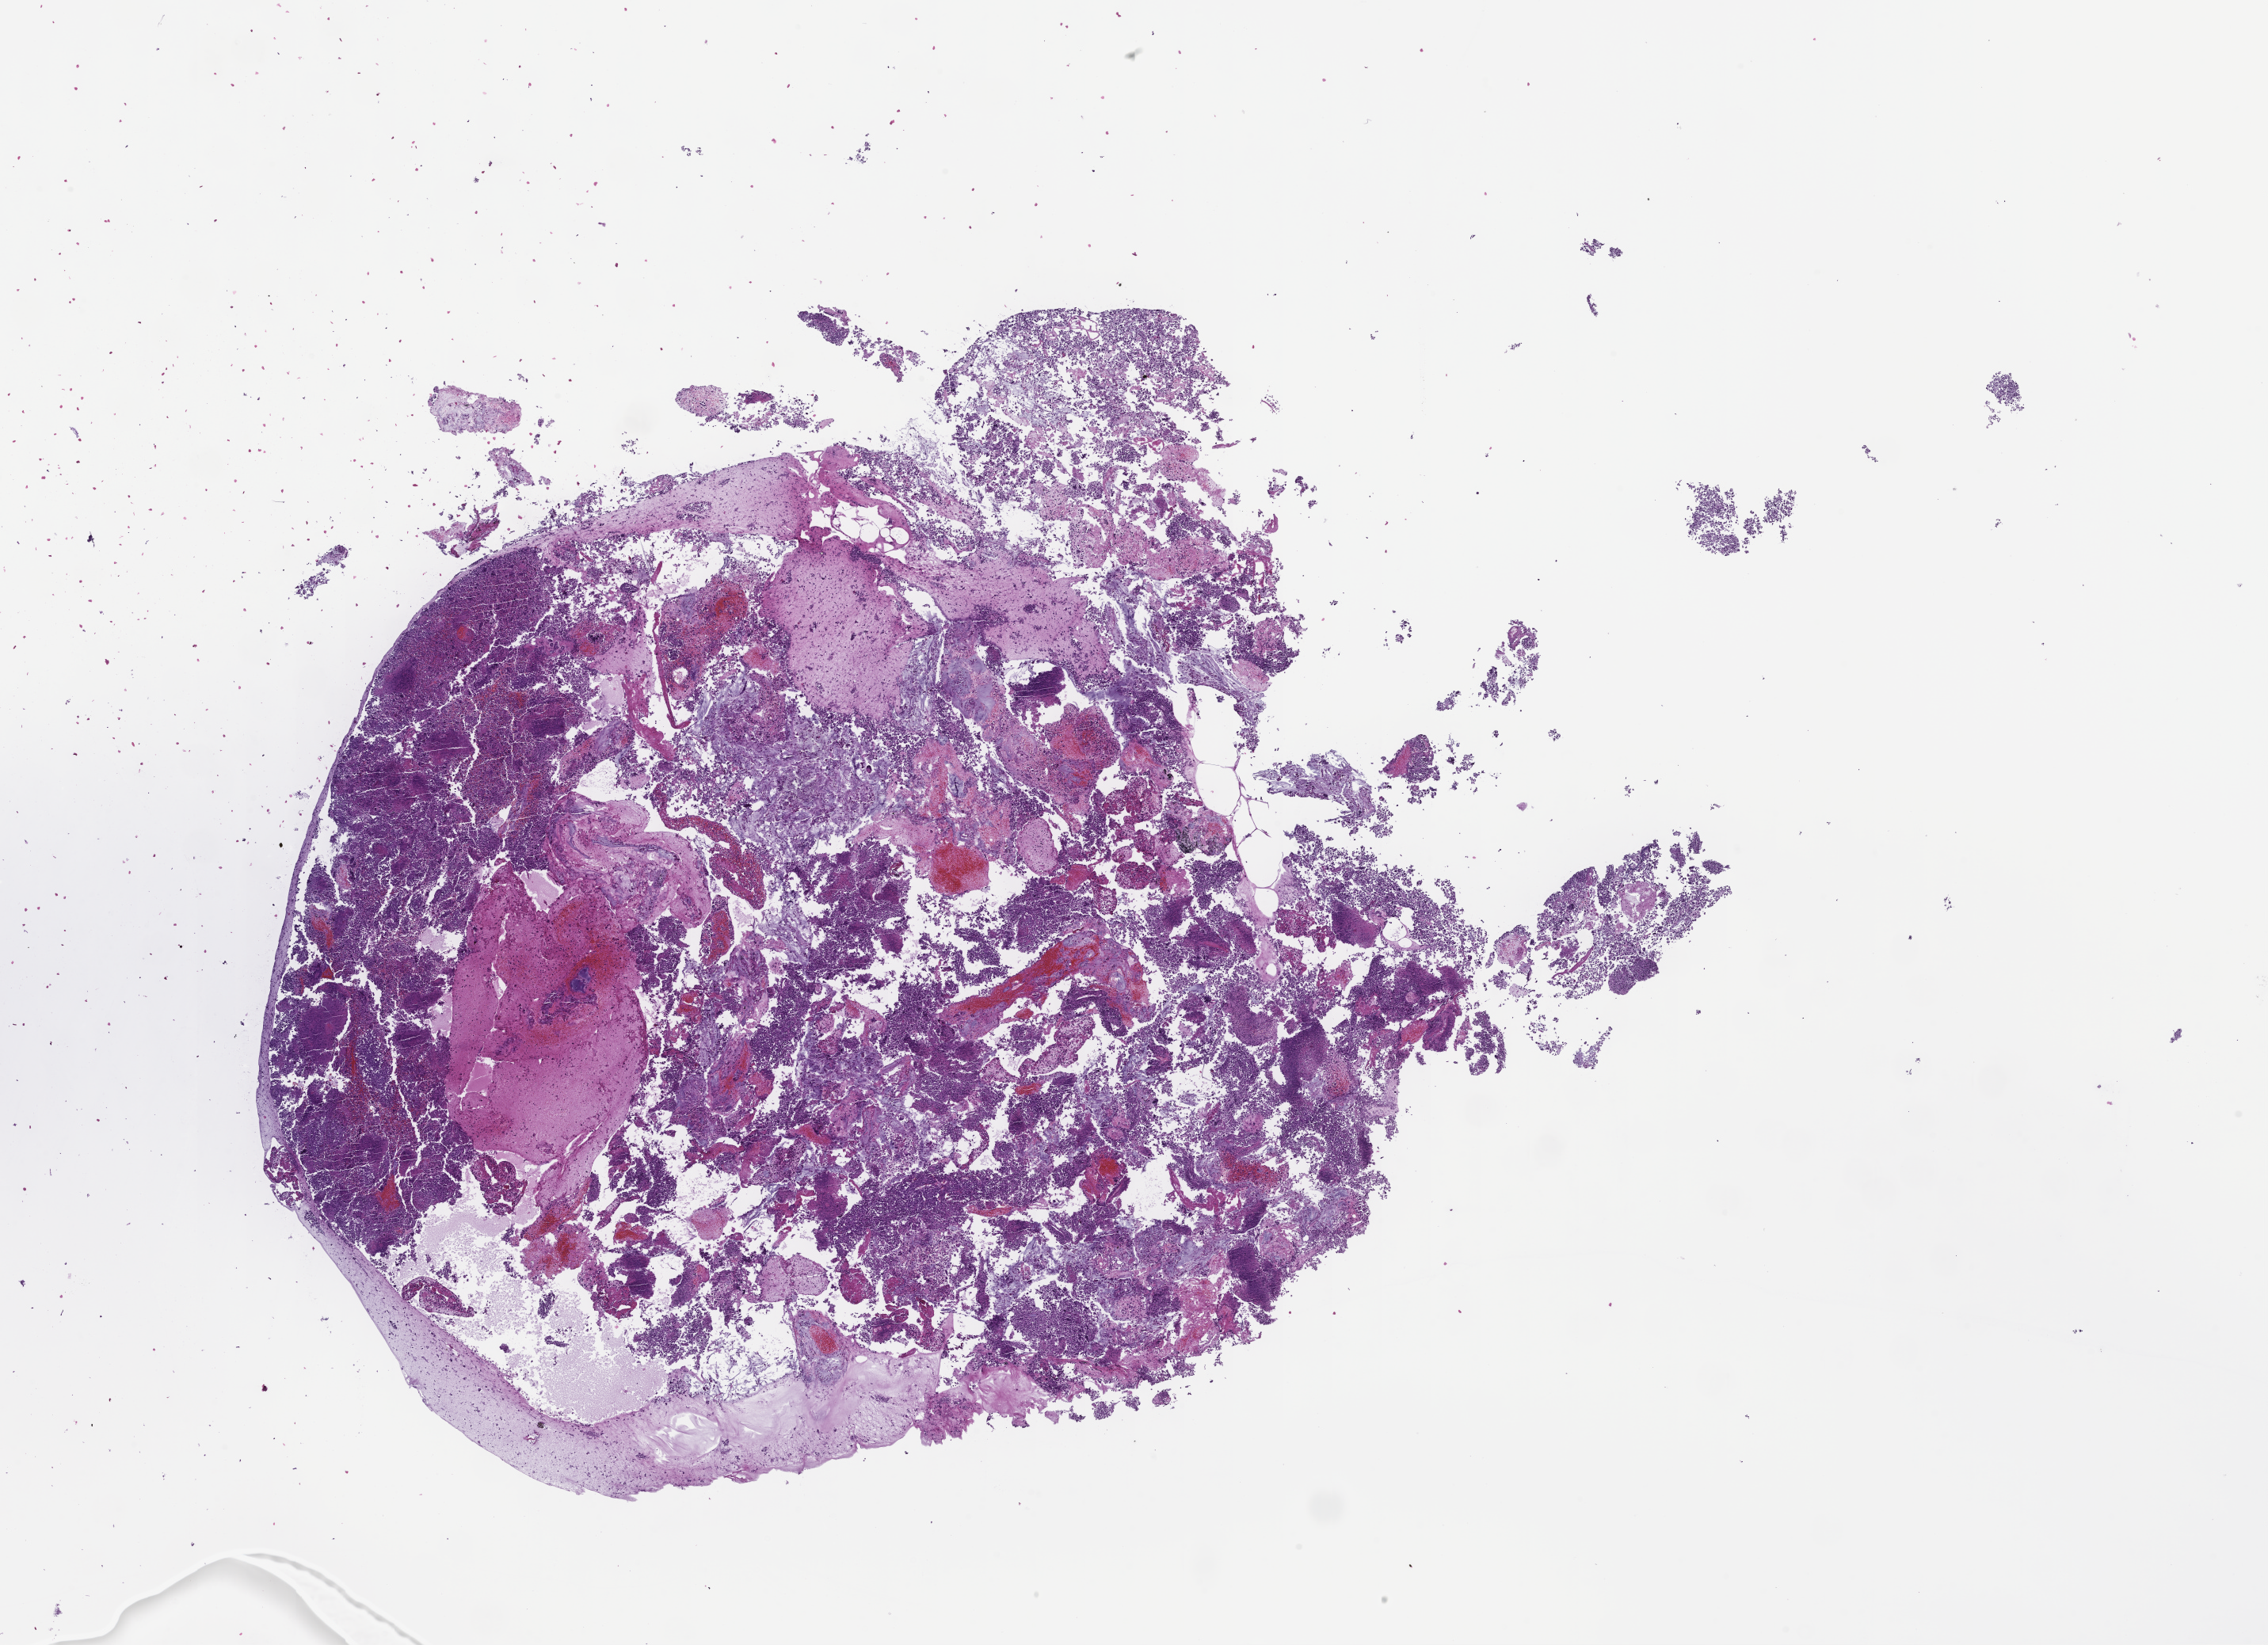
Hematoxylin and eosin (H&E) whole-slide image — whole scanned area (about 23.1 x 16.8 mm) shown as a low-resolution overview, formalin-fixed, paraffin-embedded (FFPE) tissue, tissue site: lung, specimen time point: archival tissue. Male patient.
This section: primary tumour tissue. Diagnosis: Non-Small Cell Lung Carcinoma.